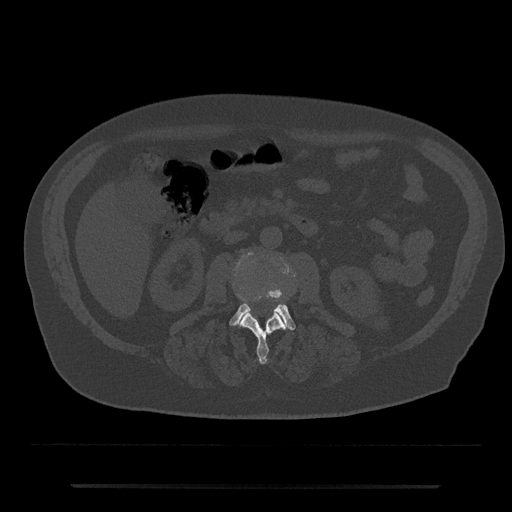
CT including the spine, one axial slice. Slice 441 of 797 in the series (ordered by position). 120 kVp. Bone window (W 1800 / L 400 HU). 0.5 mm slice thickness. 512 × 512 image matrix, field of view 434 × 434 mm. Patient: male, 80 years. From the clinical record (not read from this slice): primary cancer: prostate.
Structures marked on this image (semi-automatic segmentation, software-assisted and operator-edited):
- L2 vertebra: bounding box [x1, y1, x2, y2] px = [240, 296, 287, 364]
- L3 vertebra: [229, 288, 296, 330]